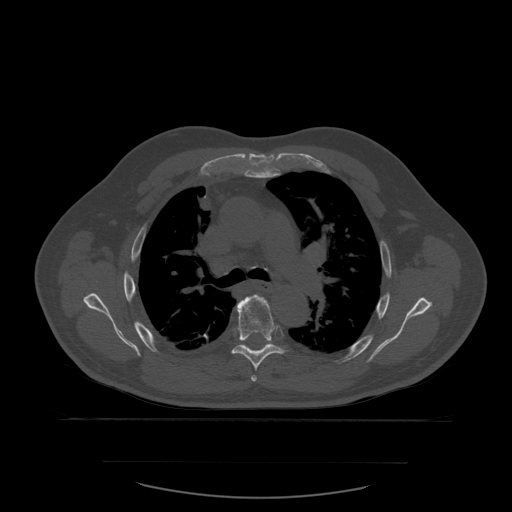
CT including the spine, one axial slice. Position 406 of 590 along the scan axis. Bone window (W 1800 / L 400 HU). 512 × 512 image matrix, field of view 479 × 479 mm. Patient age 71 years. From the clinical record (not read from this slice): primary cancer: lung; vertebrae with lytic lesions (as recorded): T1, T2, L5, S1.
Structures marked on this image (semi-automatic segmentation, software-assisted and operator-edited):
- T5 vertebra: bounding box <251,295,258,382> (left, top, right, bottom; pixels)
- T6 vertebra: <220,295,292,372>
- T7 vertebra: <249,346,266,351>